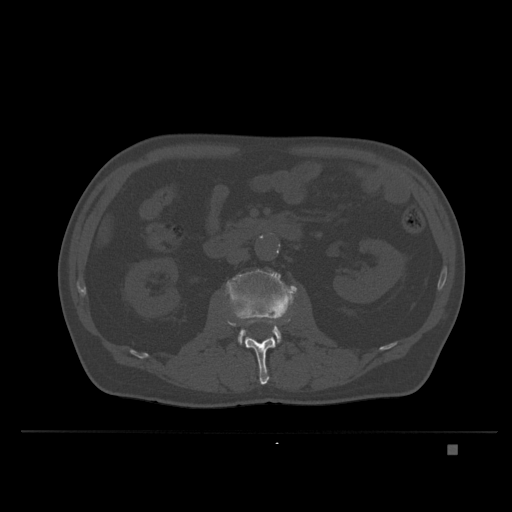
CT including the spine, one axial slice. Position 109 of 435 along the scan axis. Bone window (W 1800 / L 400 HU). 1.5 mm slice thickness. 512 × 512 image matrix. Patient: male, 73 years. From the clinical record (not read from this slice): primary cancer: skin.
Annotated regions visible in this slice (semi-automatically segmented with operator editing):
- L2 vertebra: bounding box [x1, y1, x2, y2] px = [228, 318, 289, 385]
- L3 vertebra: [226, 269, 298, 346]